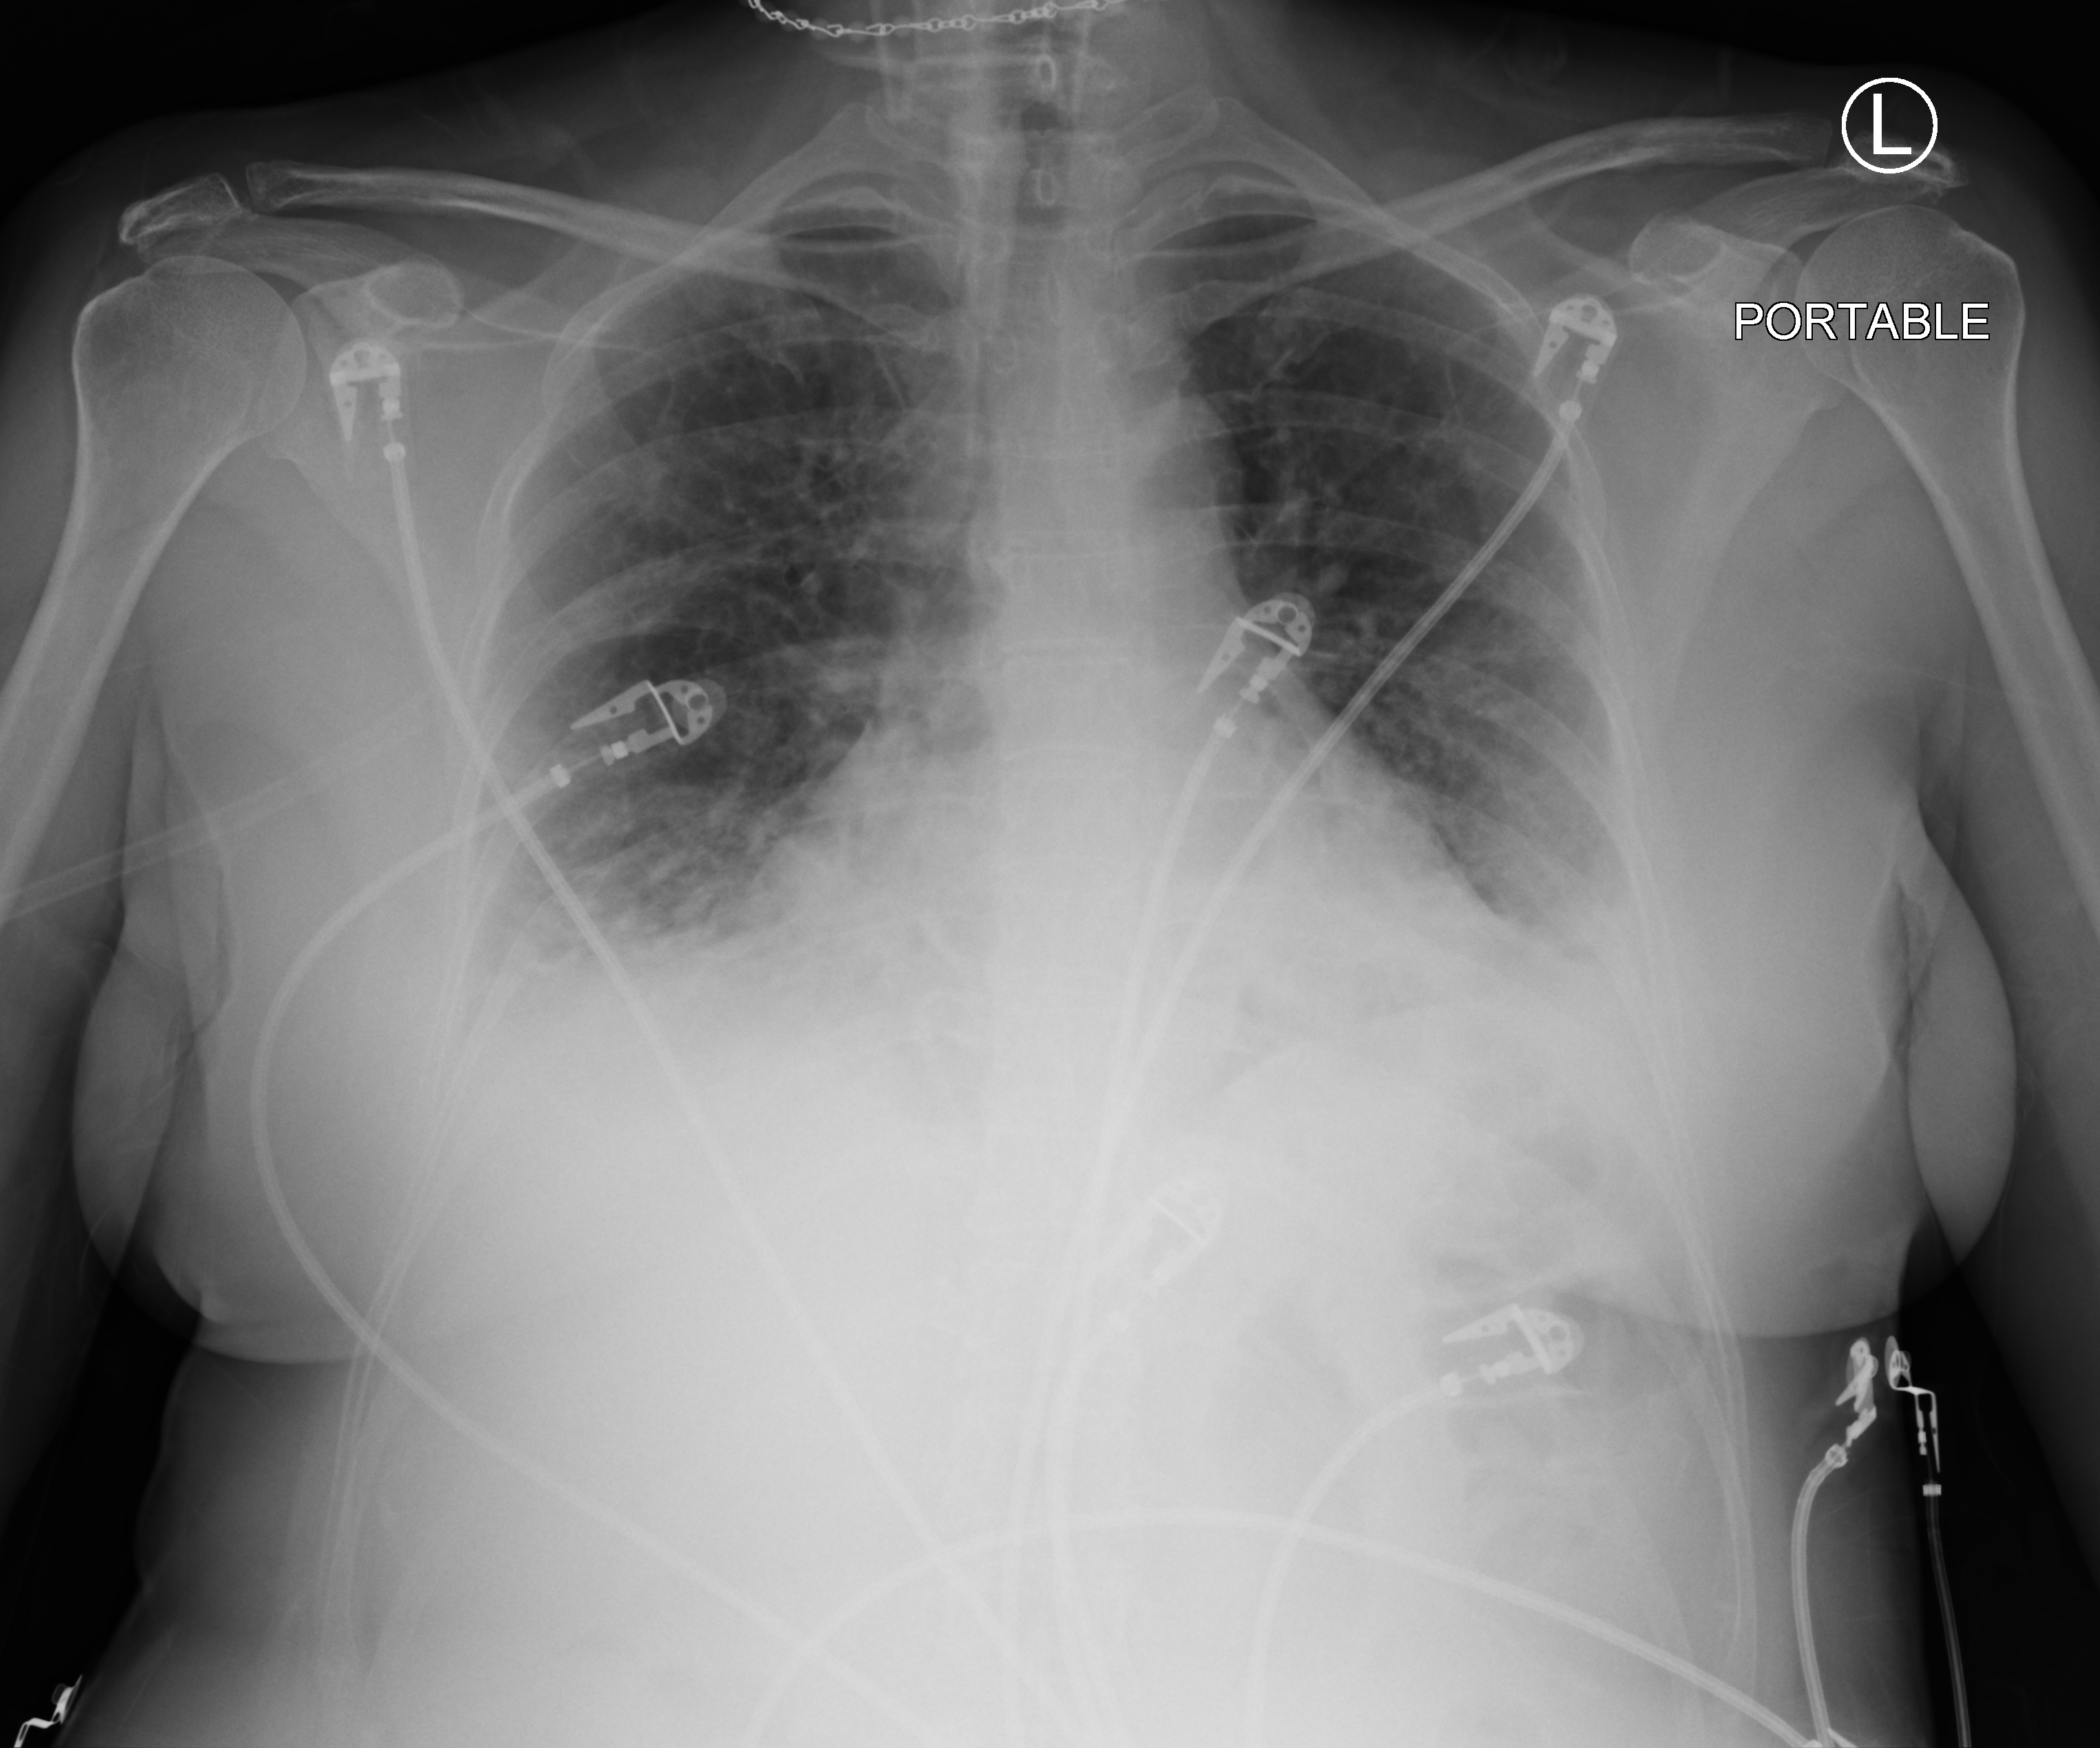
Bedside chest radiograph (computed radiography), anteroposterior (AP) projection. Female patient hospitalised with COVID-19, age 60–74 years.
Admission-level facts for this patient (not findings on this image; timing relative to this image not recorded): admitted to intensive care during this hospital stay: no.